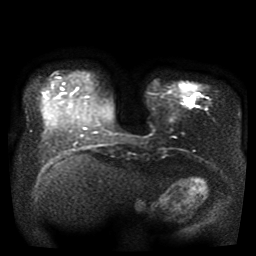
Breast MRI, one axial slice. Slice 8 of 41 in the series (ordered by position). Diffusion-weighted series; image 2 of 4 stored at this slice position (different b-values; order by instance number). 1.5 T. 5 mm slice thickness. 256 × 256 image matrix. Female patient.
Outlined on this slice (outlined manually by an expert reader):
- tumour on diffusion-weighted imaging: bounding box (x1, y1, x2, y2) in pixels: (188, 99, 194, 105)